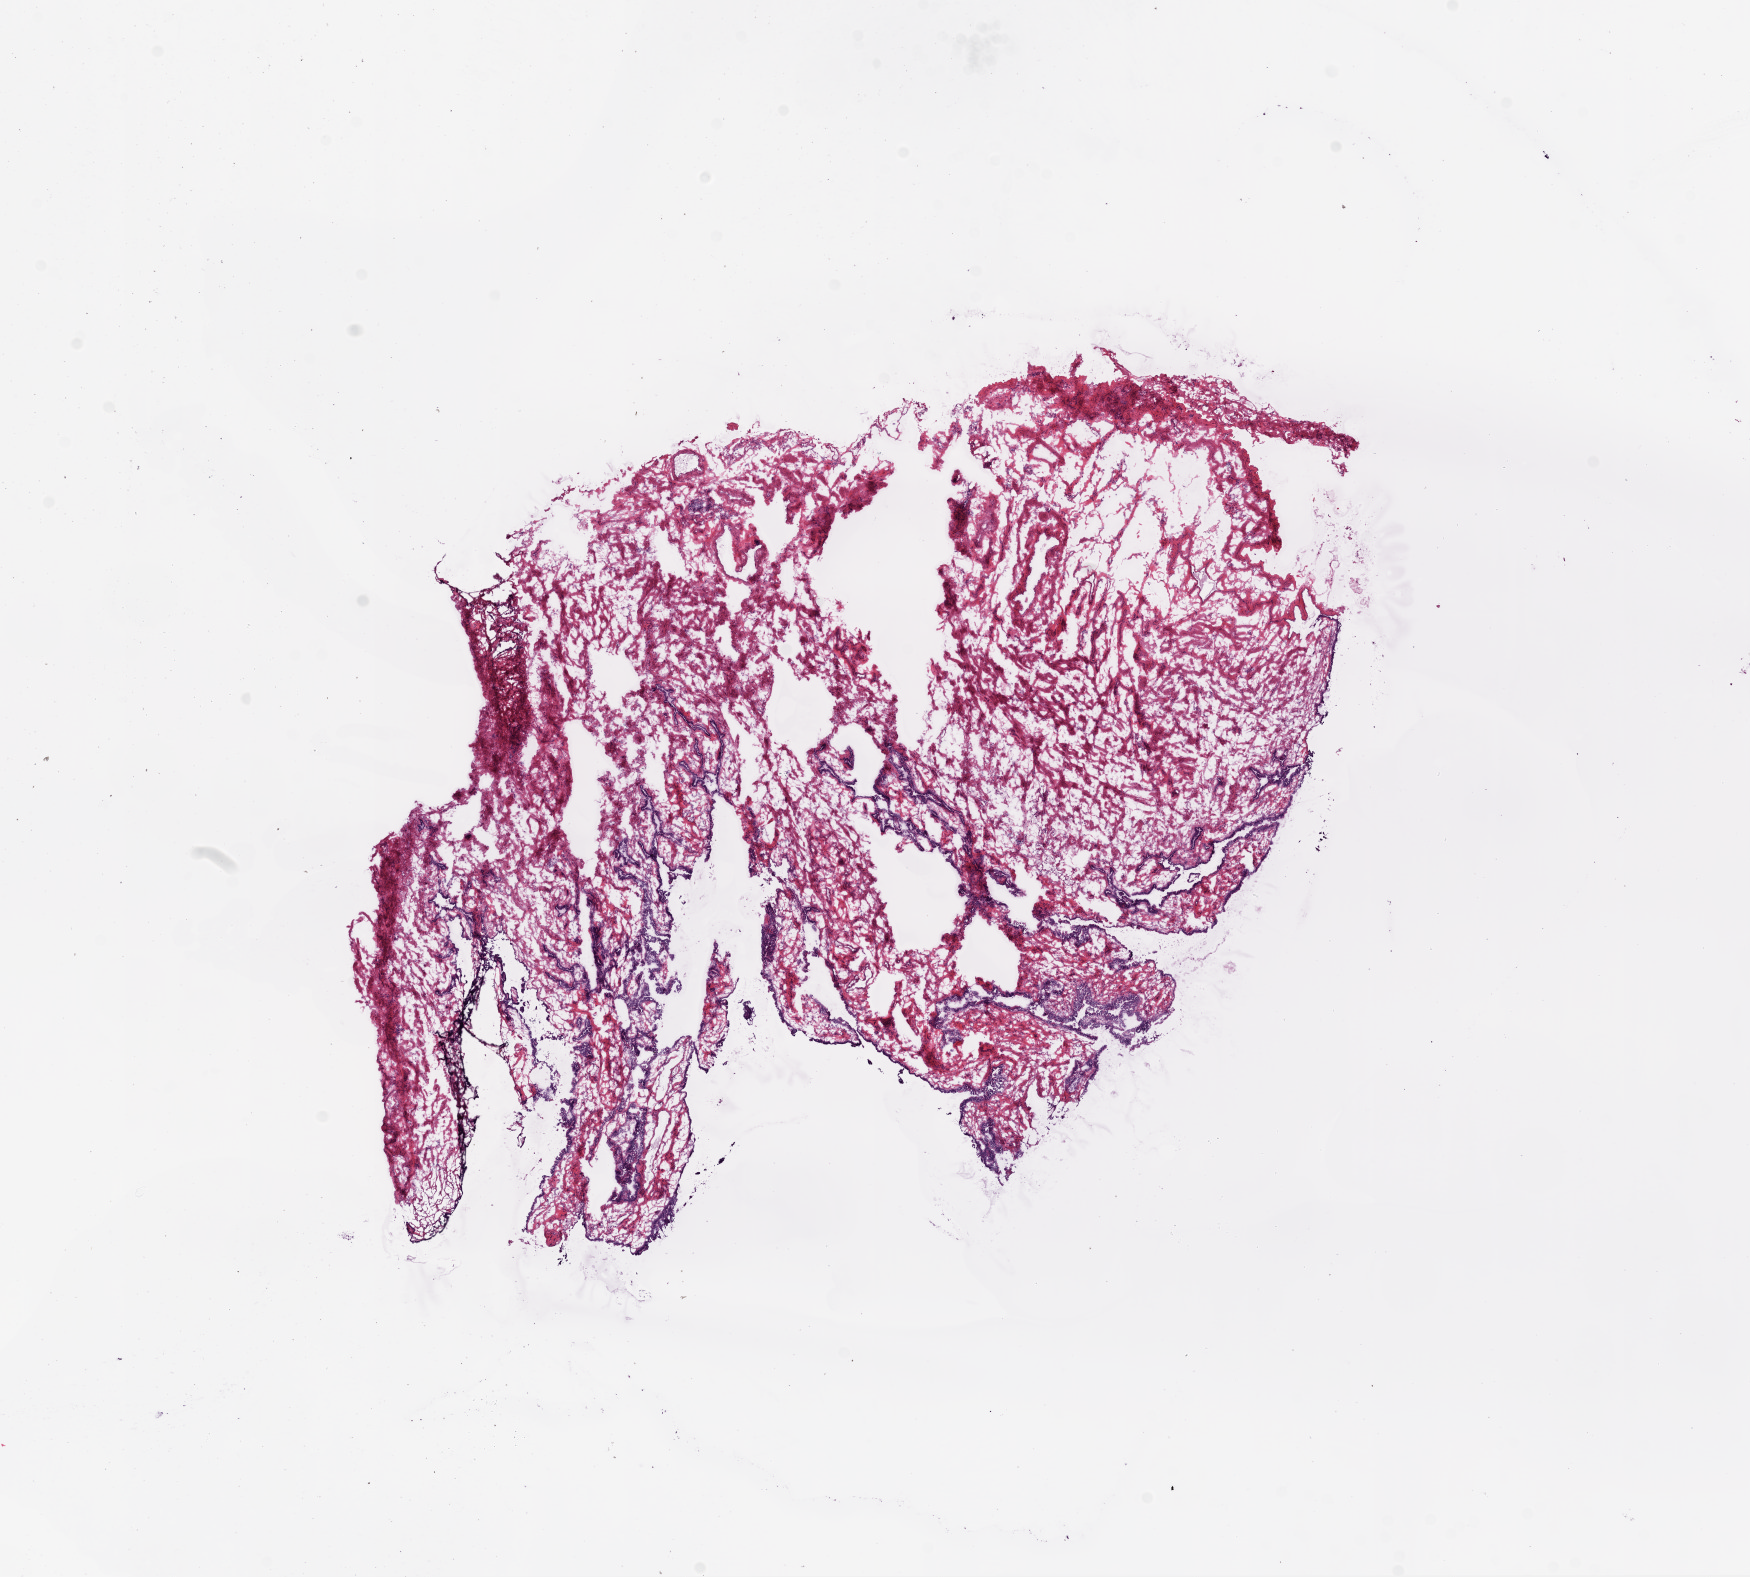
Whole-slide histology image, H&E — whole scanned area (about 14.0 x 12.7 mm) shown as a low-resolution overview. Frozen section from the bottom of the tissue portion. Ovary, solid tissue normal (non-tumour tissue) sample. Female patient; age at initial diagnosis 62 years.
This section: solid tissue normal (non-tumour) sample from the same patient. Patient diagnosis: Serous cystadenocarcinoma, NOS.